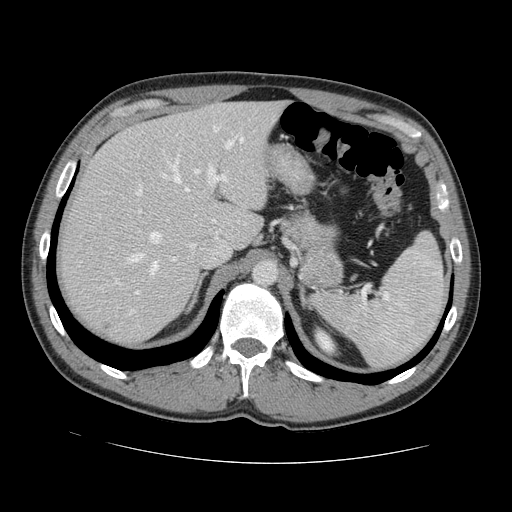
Contrast-enhanced abdominal CT, one axial slice; slice 95 of 131 in the series (ordered by position); soft-tissue window (W 400 / L 40 HU); 512 × 512 image matrix. Male patient, age 40 years. Case-level facts recorded for this patient, not image findings: diagnosis: colorectal cancer liver metastases, imaged before liver resection; multiple liver metastases: yes; largest metastasis: 2.9 cm; disease in both lobes: yes.
Annotated regions visible in this slice (manually delineated by an expert):
- hepatic veins: box from (x=129, y=137) to (x=243, y=314) px
- liver: (x=62, y=102)–(x=282, y=345)
- planned liver remnant (the part of the liver to remain after resection): (x=99, y=102)–(x=283, y=247)
- portal vein (with intrahepatic branches): (x=135, y=138)–(x=236, y=295)
- liver metastasis: (x=106, y=325)–(x=111, y=329)